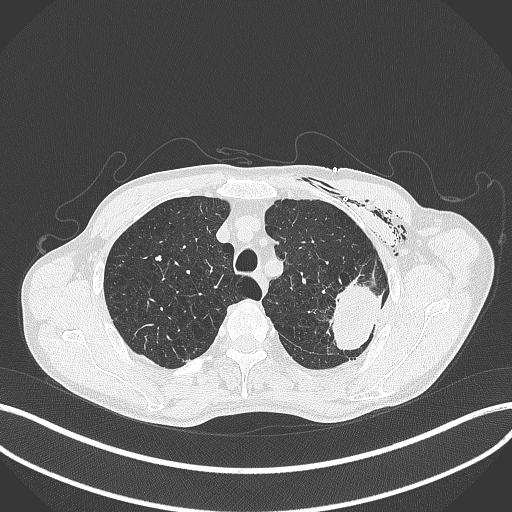
Chest CT, one axial slice. Position 328 of 457 along the scan axis. 120 kVp. Lung window (W 1500 / L -600 HU). 1 mm slice thickness. 512 × 512 image matrix, field of view 400 × 400 mm. Male patient, age 58 years. Case-level facts recorded for this patient, not image findings: clinical TNM (as recorded): T3 N0 M0.
Structures marked on this image (bounding box drawn by a radiologist):
- lung tumour (recorded histology: adenocarcinoma): bounding box <323,276,382,352> (left, top, right, bottom; pixels)